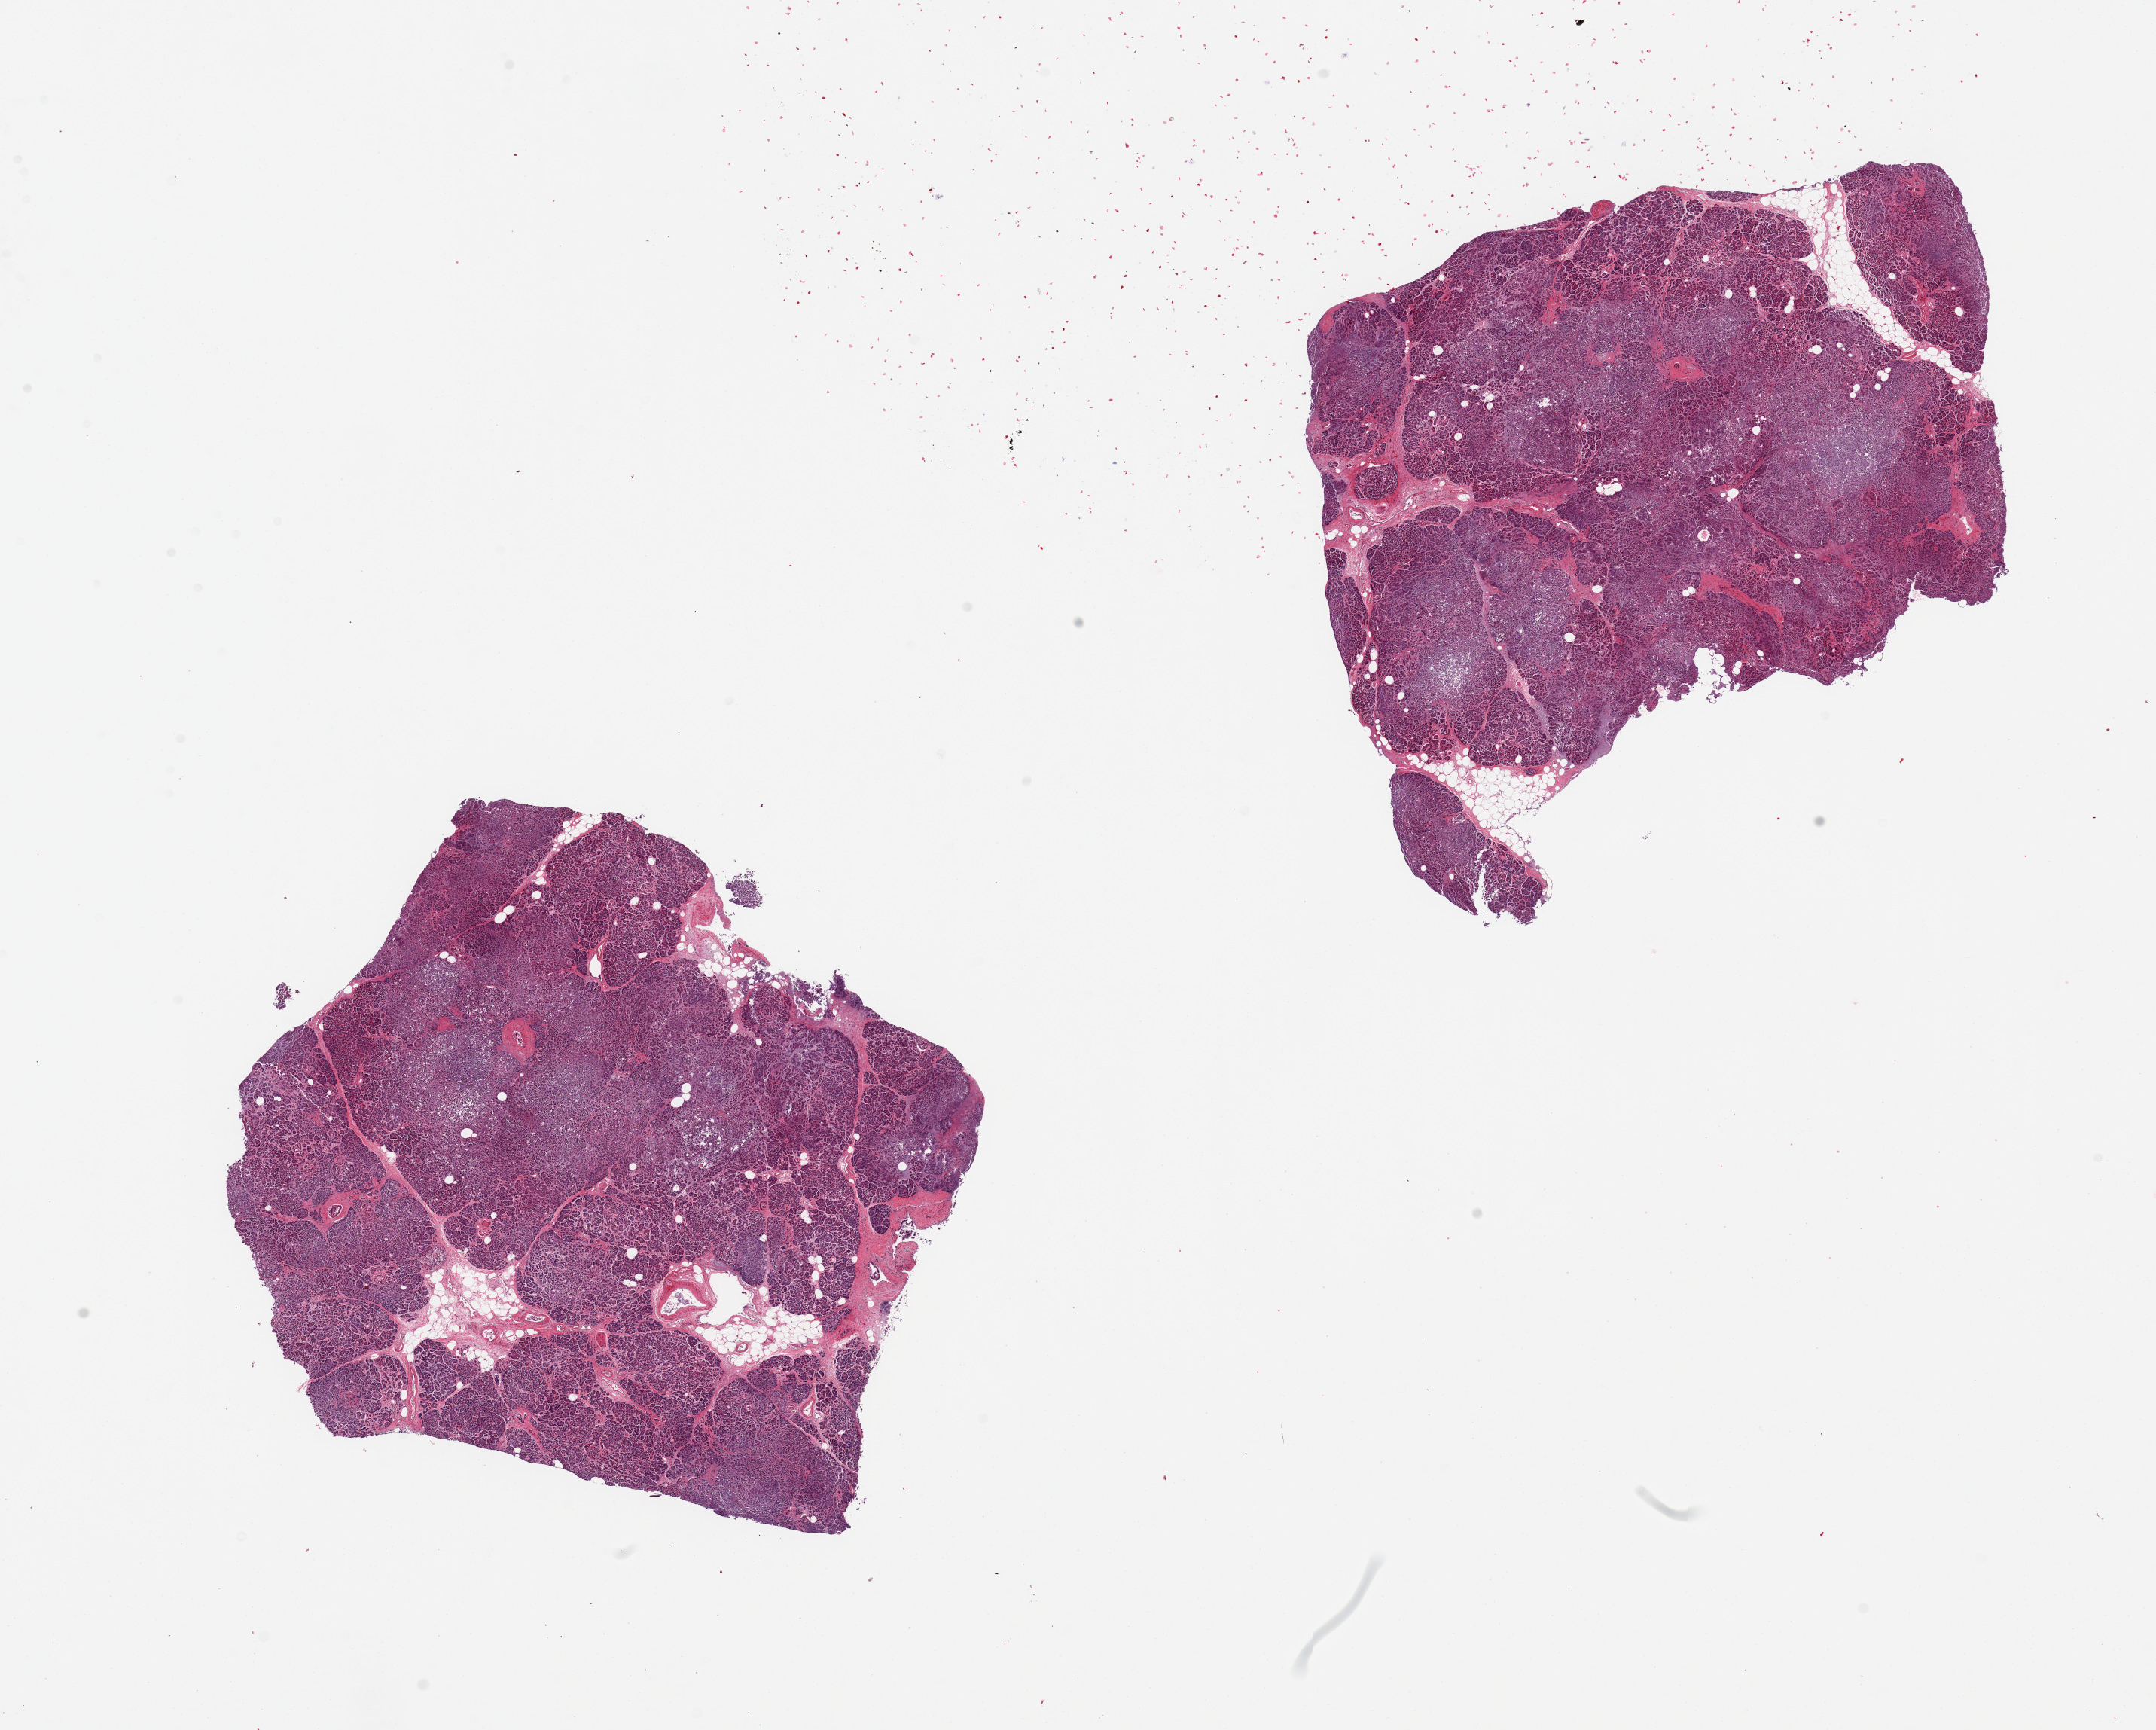
Whole-slide image, haematoxylin and eosin stain, shown as a low-resolution overview of the whole scanned area (about 22.6 x 18.2 mm, slide scanned at 20x), PAXgene-fixed paraffin-embedded (PFPE) section, section of pancreas (target tissue), donor tissue sample.
Reviewer comment on this tissue sample: 2 pieces; perilobular fibrosis and parenchymal autolysis; small amounts of internal and external fat.